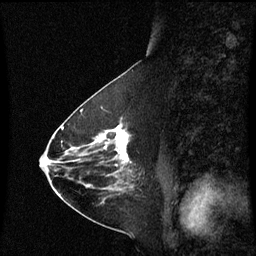
Breast MRI (dynamic contrast-enhanced), one sagittal slice. Slice 28 of 60 in the series (ordered by position). Dynamic contrast-enhanced series, image 2 of 3 at this slice position (ordered by acquisition). 1.5 T. TE 4.2 ms, TR 8.9 ms. 2 mm slice thickness. 256 × 256 image matrix. Patient: female, 63 years. Case-level facts recorded for this patient, not image findings: setting: breast cancer imaged before/during neoadjuvant chemotherapy; receptor status: HR-positive, HER2-negative.
Outlined on this slice (semi-automatic segmentation, software-assisted and operator-edited):
- analysis volume of interest (the breast-tissue region the enhancement analysis was run in; not a lesion): bounding box (x1, y1, x2, y2) in pixels: (94, 122, 133, 177)
- tumour enhancement mask (voxels above the 70 % enhancement threshold inside the analysis volume of interest): (99, 126, 130, 161)